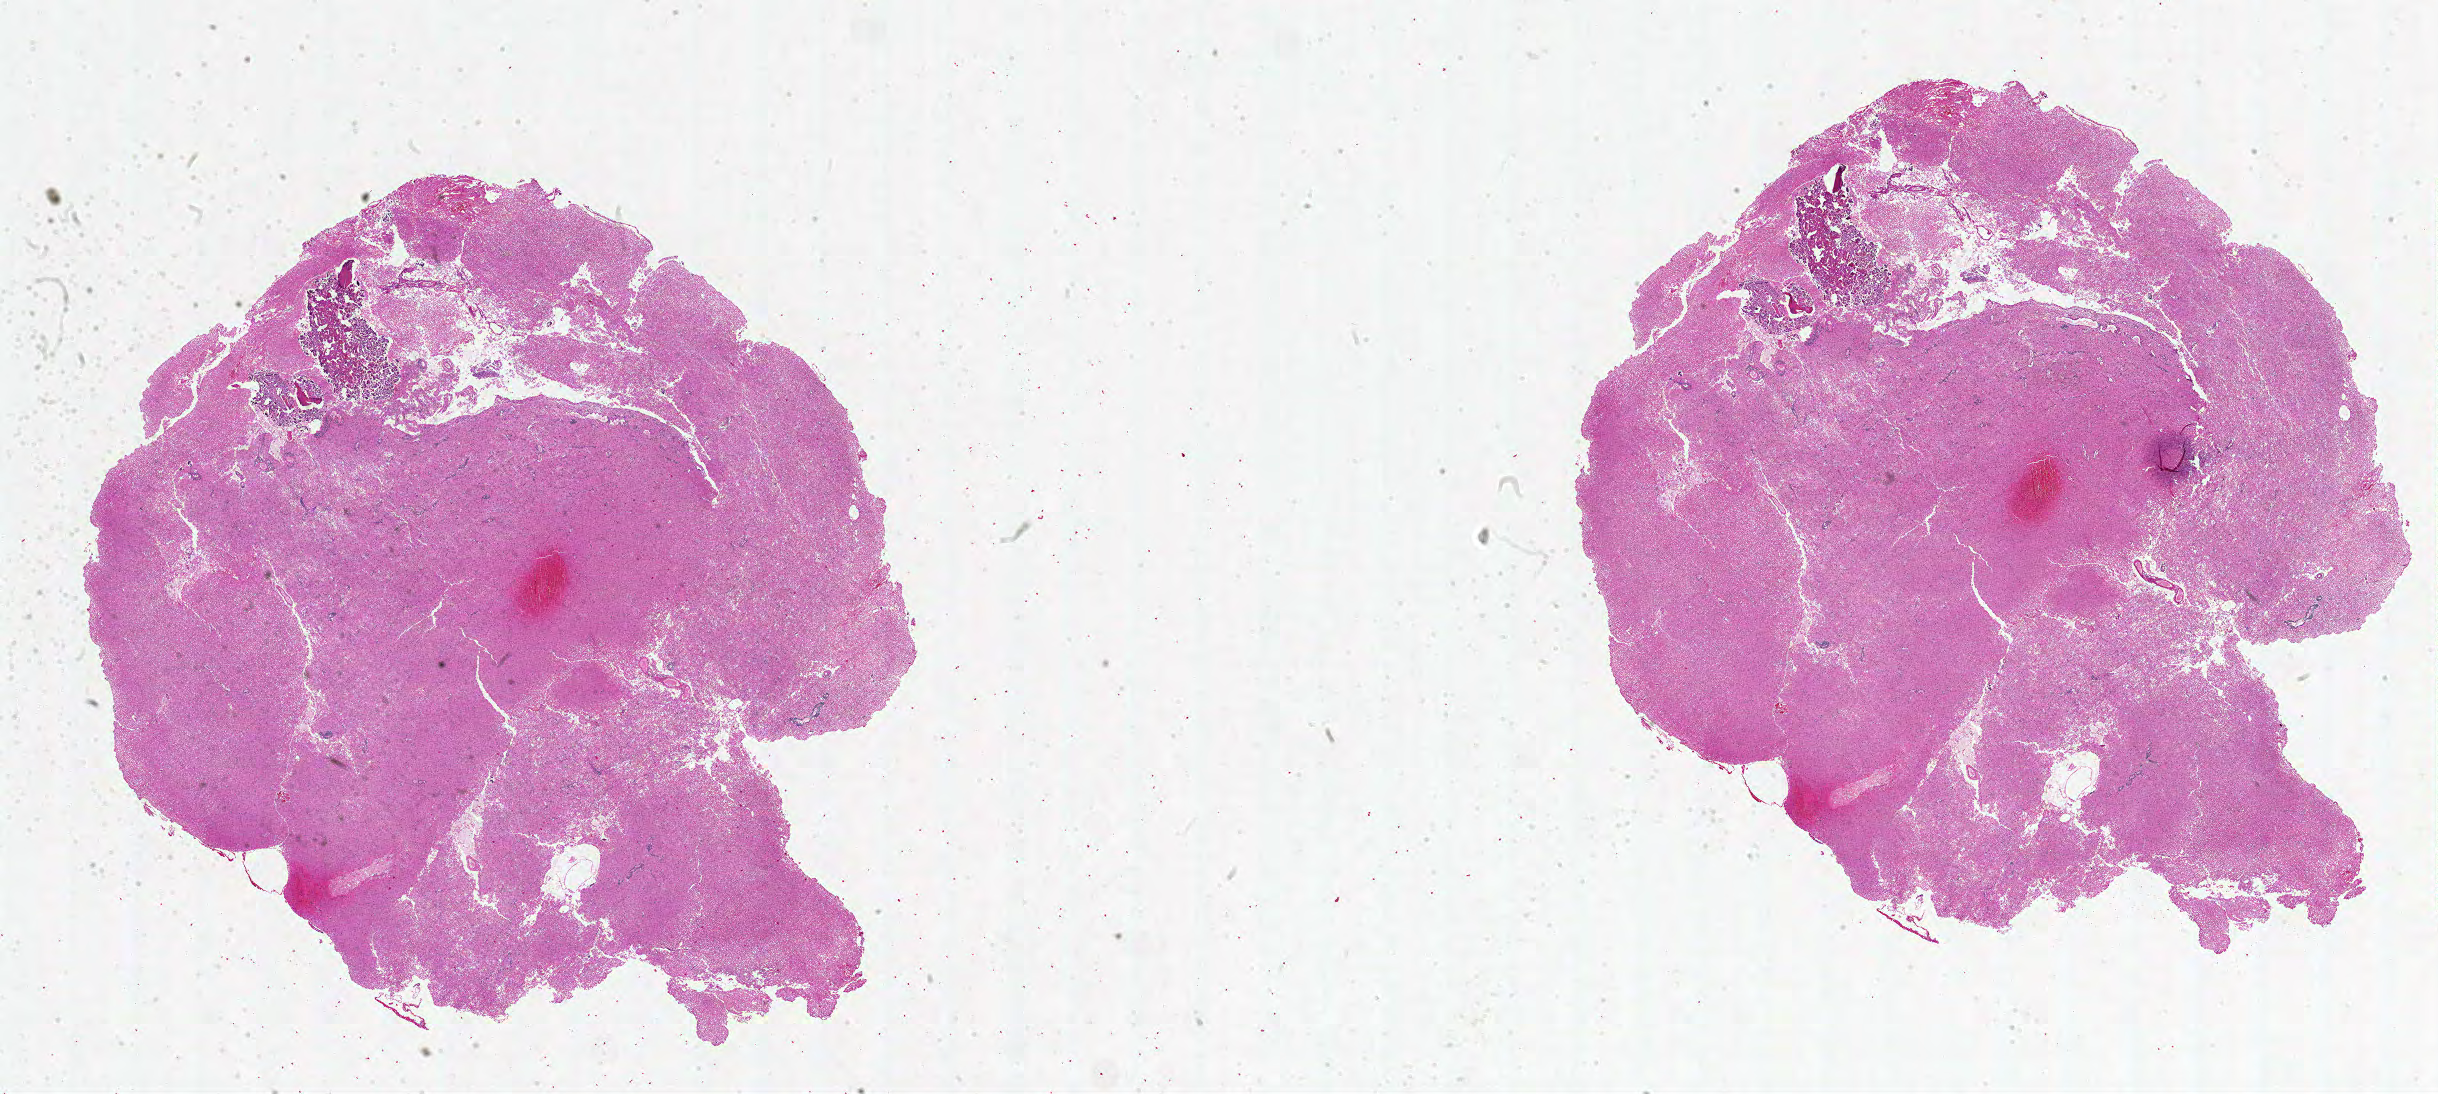
Whole-slide histology image, H&E-stained — whole scanned area (about 39.0 x 17.5 mm, acquisition: 20x scan) shown as a low-resolution overview; formalin-fixed paraffin-embedded (FFPE) diagnostic section; brain, primary tumour sample. Patient: male, age at initial diagnosis 60 years.
Pathologic diagnosis: Glioblastoma.